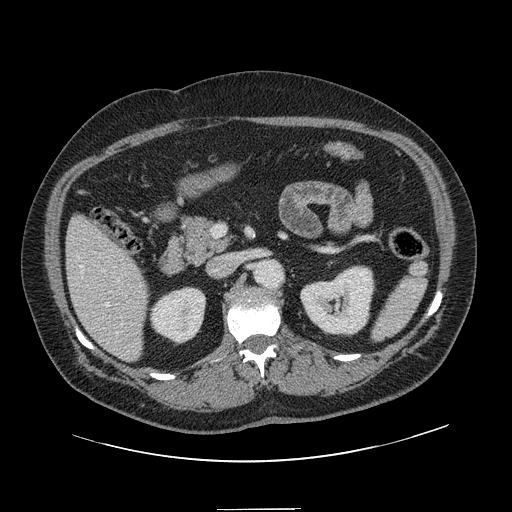
Contrast-enhanced abdominal CT, one axial slice; slice 62 of 154 in the series (ordered by position); soft-tissue window (W 400 / L 40 HU); 2.5 mm slice thickness; 512 × 512 image matrix. Male patient, age 61 years. Case-level facts recorded for this patient, not image findings: diagnosis: colorectal cancer liver metastases, imaged before liver resection; multiple liver metastases: yes; largest metastasis: 2.6 cm; disease in both lobes: yes.
Outlined on this slice (outlined manually by an expert reader):
- hepatic veins: box from (x=80, y=265) to (x=118, y=334) px
- liver: (x=68, y=217)–(x=148, y=361)
- planned liver remnant (the part of the liver to remain after resection): (x=68, y=217)–(x=149, y=361)